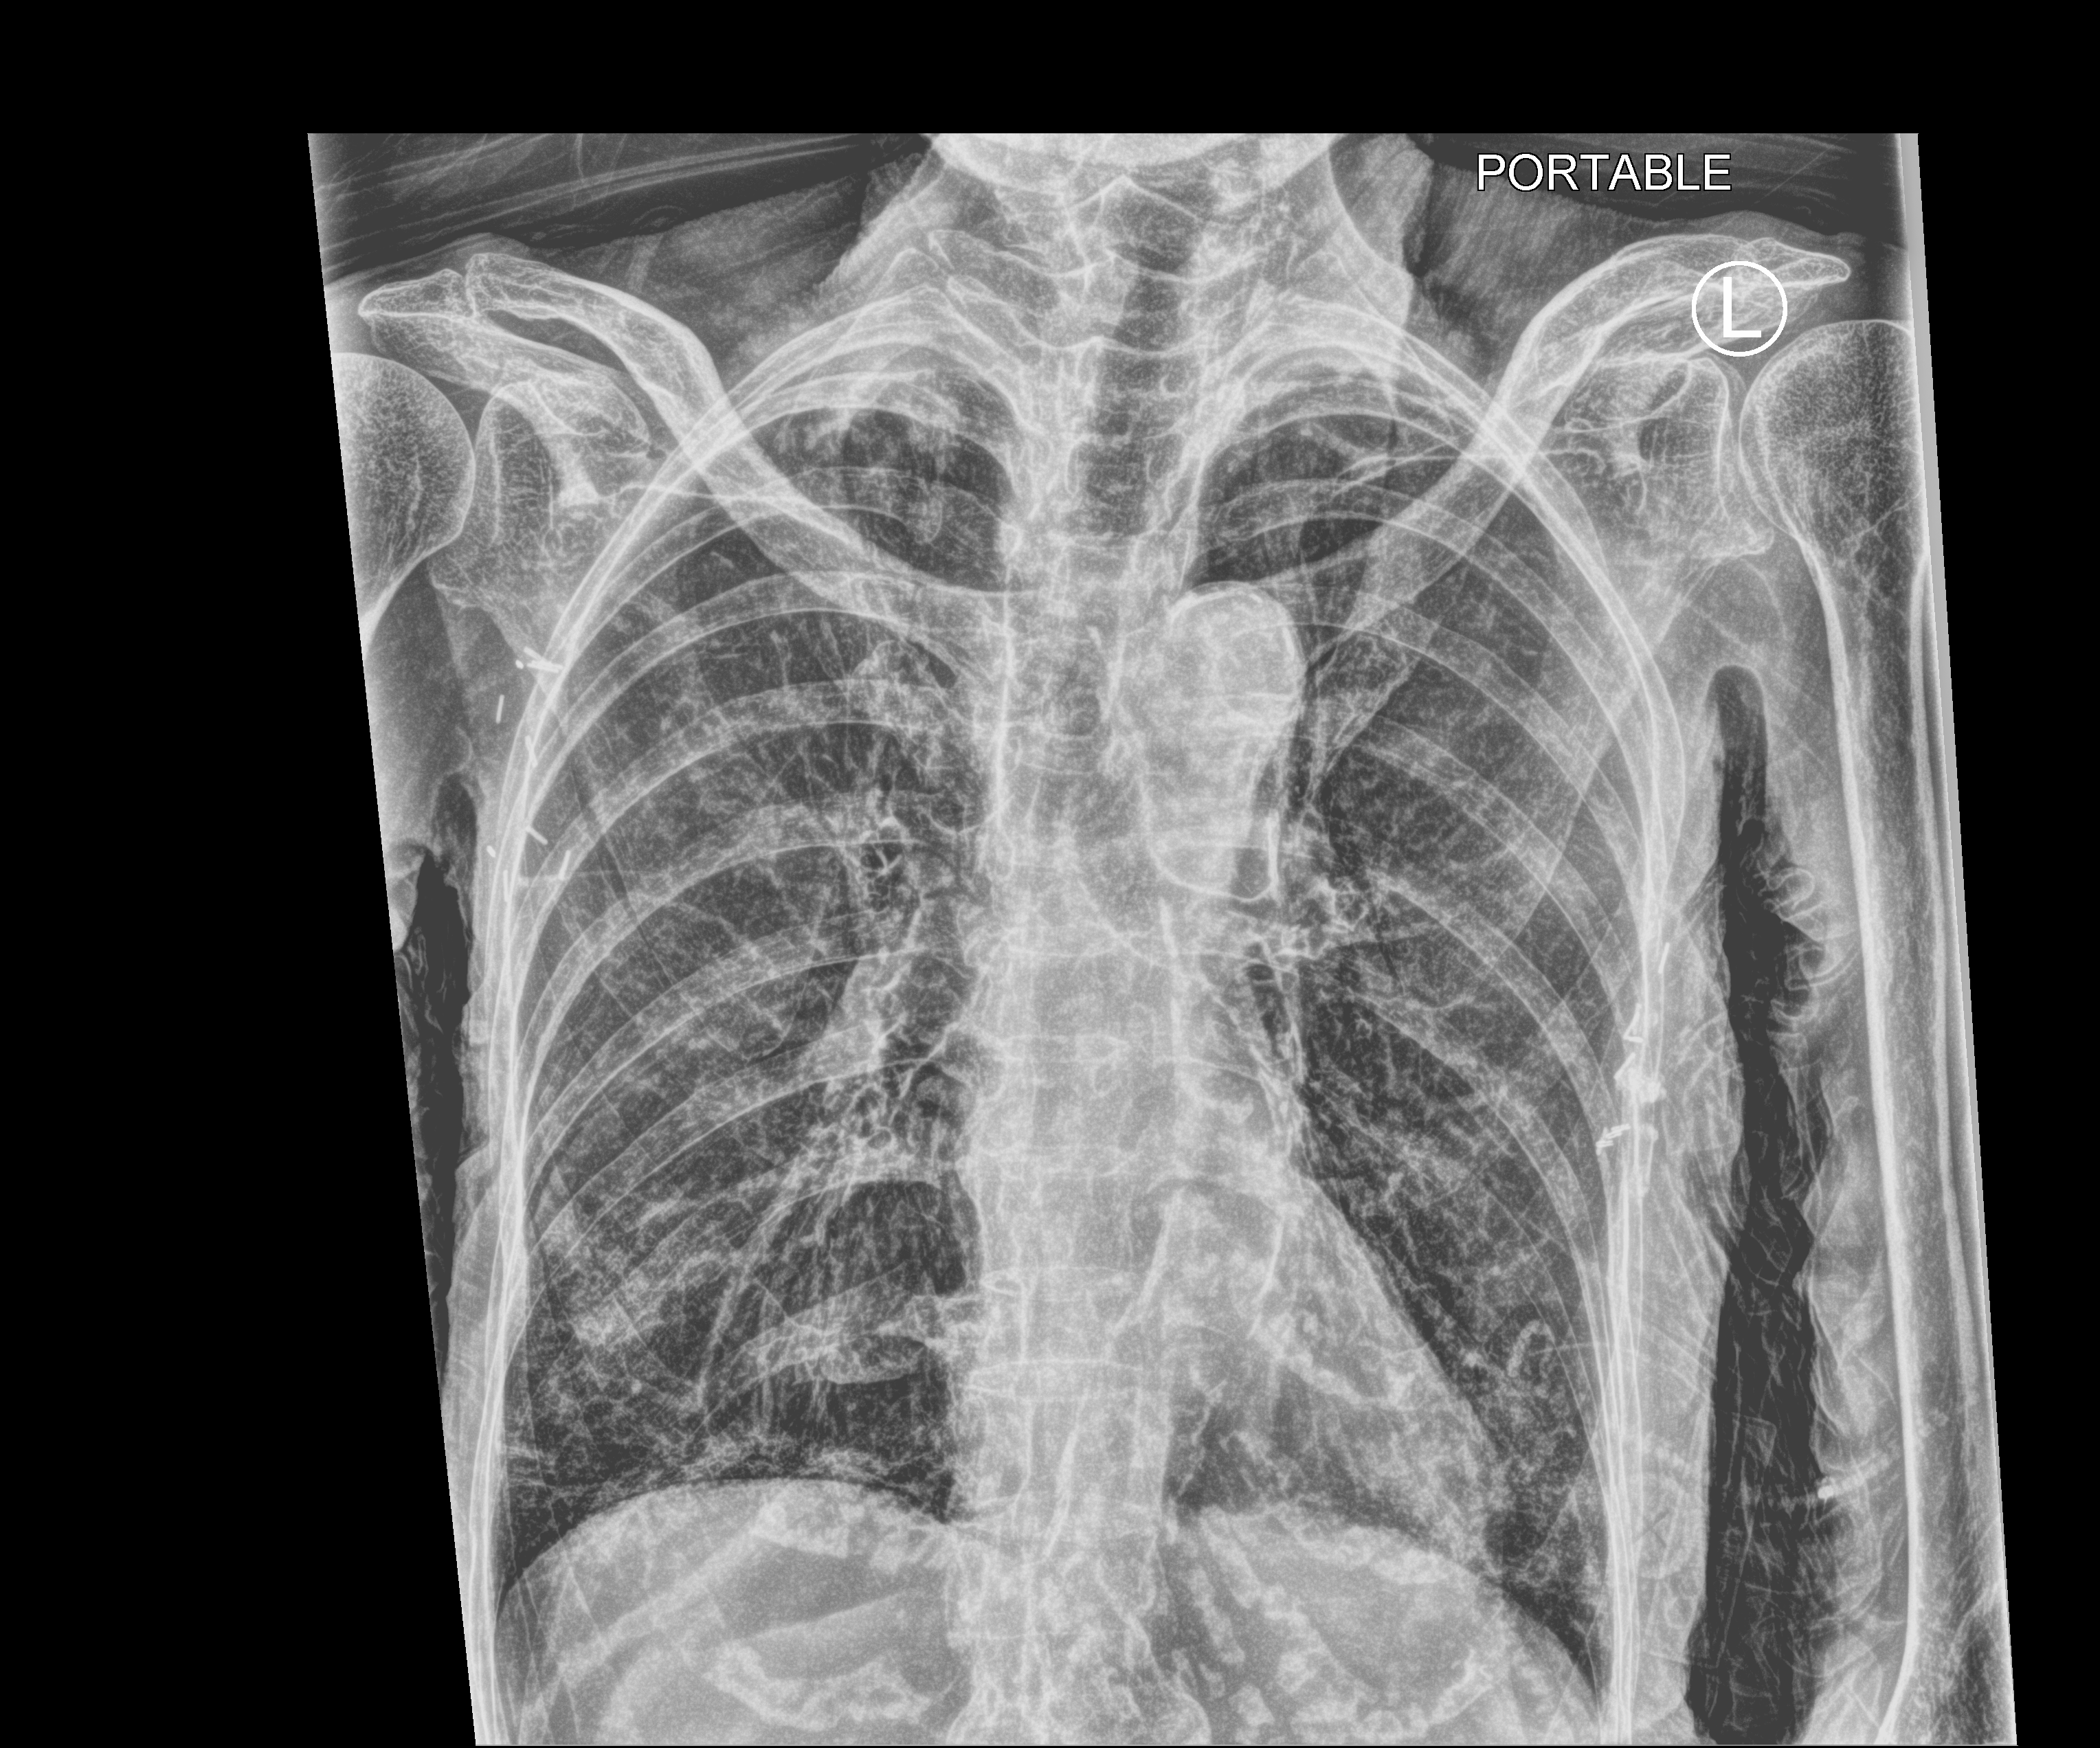
Bedside chest radiograph (computed radiography), anteroposterior (AP) projection. Female patient hospitalised with COVID-19, age 75–90 years.
From the hospital-stay record, not from the radiograph (when in the stay this image was taken is not recorded):
- admitted to intensive care during this hospital stay: no
- mechanically ventilated during this hospital stay: no